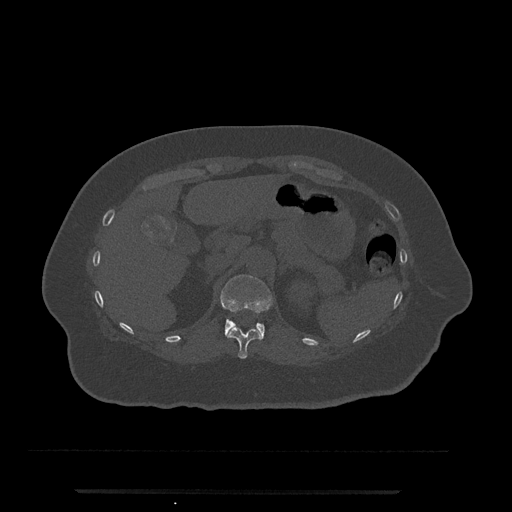
CT including the spine, one axial slice. Slice 199 of 797 in the series (ordered by position). Reconstruction kernel Br40s/3. 120 kVp. Bone window (W 1800 / L 400 HU). 512 × 512 image matrix. Patient: female, 51 years. From the clinical record (not read from this slice): primary cancer: neuro; vertebrae with lytic lesions (as recorded): T8.
Annotated regions visible in this slice (semi-automatically segmented with operator editing):
- T11 vertebra: bounding box <226,327,261,359> (left, top, right, bottom; pixels)
- T12 vertebra: <221,275,273,340>